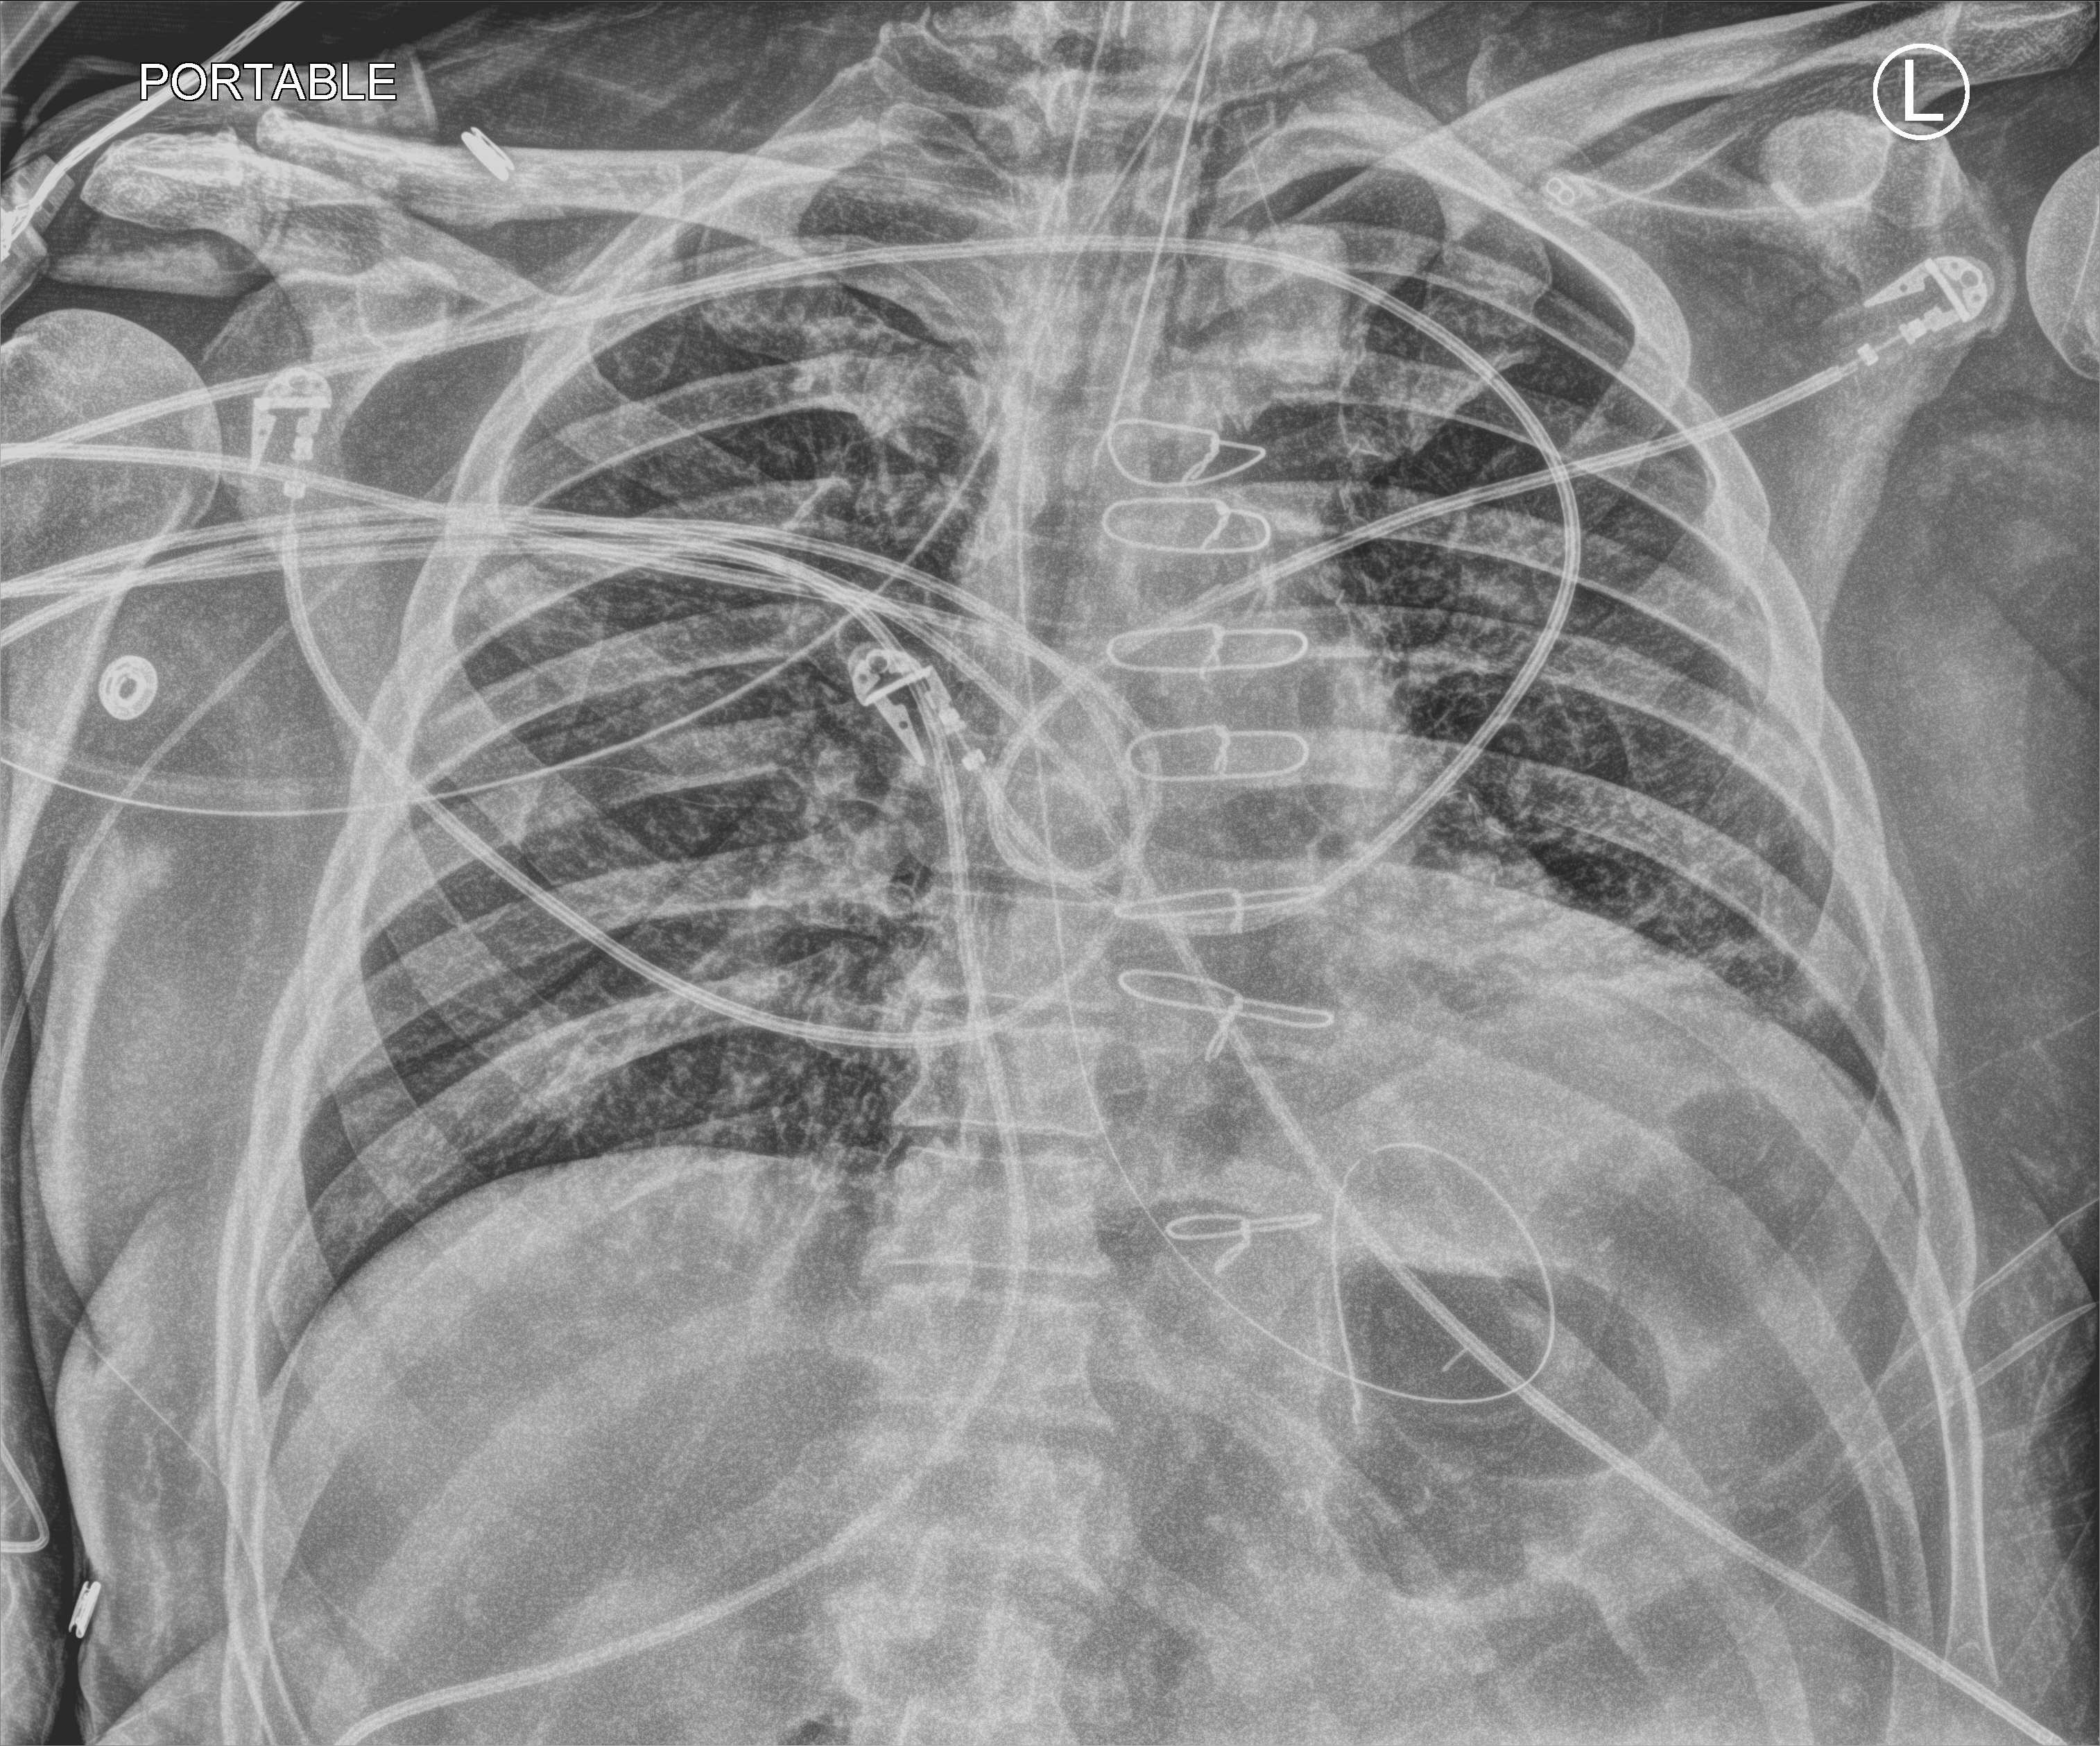
Bedside chest radiograph (computed radiography); anteroposterior (AP) projection. Patient hospitalised with COVID-19; male, aged 60–74 years.
From the hospital-stay record, not from the radiograph (when in the stay this image was taken is not recorded):
- length of hospital stay: 44 days
- mechanically ventilated during this hospital stay: yes
- admitted to intensive care during this hospital stay: yes